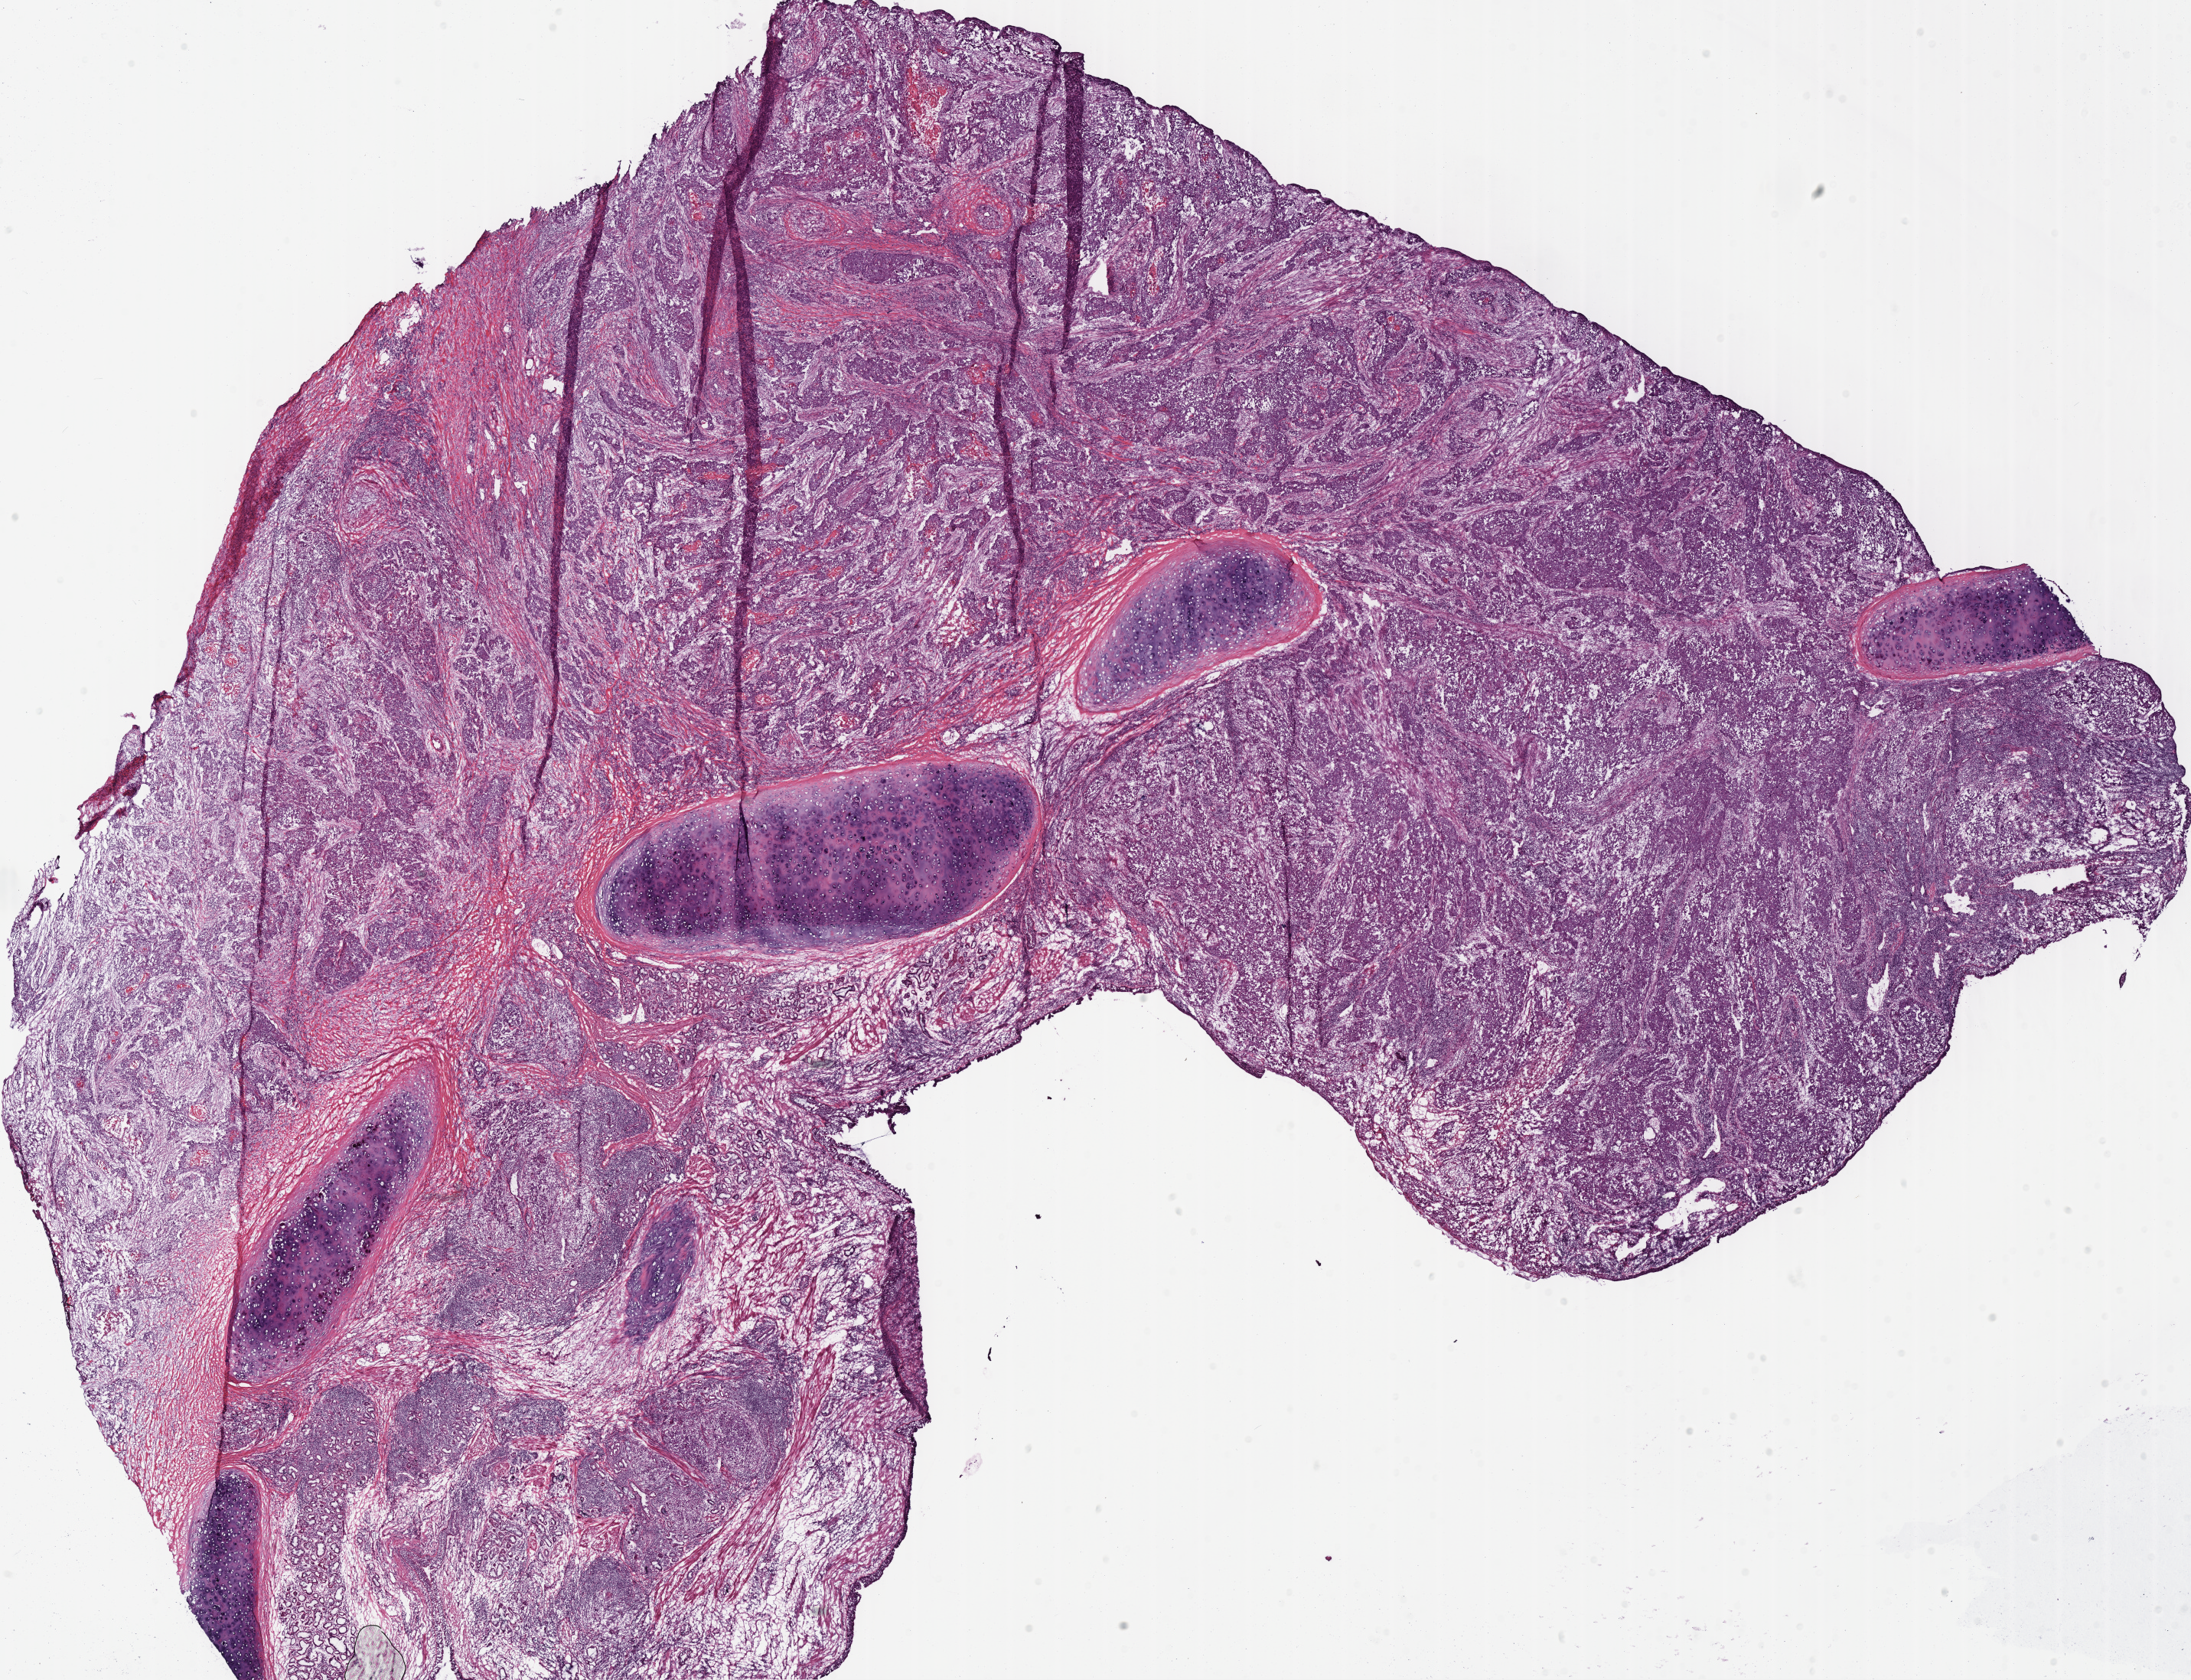
Digitized H&E-stained tissue section (whole slide), shown as a low-resolution overview of the whole scanned area (about 22.5 x 17.3 mm); frozen section; lung, primary tumour sample. Male patient; age at initial diagnosis 57 years. Composition of this section per pathologist review: tumour cells 60%, tumour nuclei 60%, normal cells 25%, stromal cells 15%, necrosis 0%. Infiltration values recorded for this section: lymphocyte infiltration 30%.
TNM: T2a N0 M0. Histologic diagnosis: Squamous cell carcinoma, NOS (lower lobe, lung). AJCC pathologic stage: IB (7th edition).